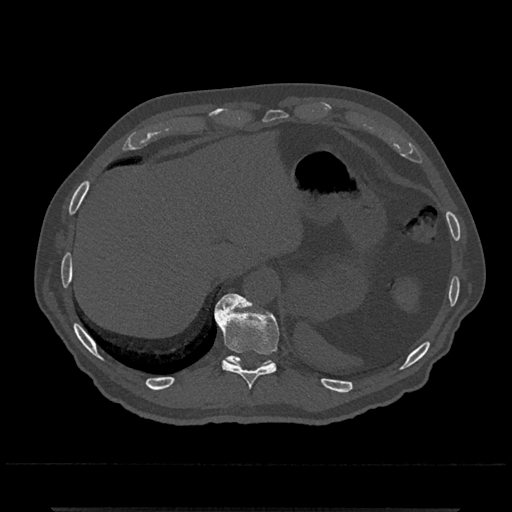
CT including the spine, one axial slice; slice 540 of 797 in the series (ordered by position); 120 kVp; bone window (W 1800 / L 400 HU); 0.5 mm slice thickness; 512 × 512 image matrix. Patient: male, 67 years. From the clinical record (not read from this slice): primary cancer: prostate.
Annotated regions visible in this slice (semi-automatic segmentation, software-assisted and operator-edited):
- T10 vertebra: bounding box [x1, y1, x2, y2] px = [214, 293, 279, 389]
- T11 vertebra: [224, 298, 273, 367]